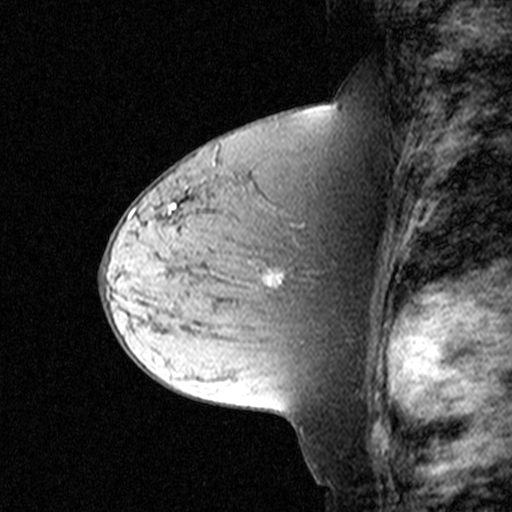
Breast MRI (dynamic contrast-enhanced), one sagittal slice. Position 21 of 44 along the scan axis. Dynamic contrast-enhanced study with each time point stored as its own series, time point 2 of 3 at this slice position (early post-contrast, ordered by acquisition time). 1.5 T. TE 4.5 ms, TR 11 ms. 3 mm slice thickness. 512 × 512 image matrix, field of view 200 × 200 mm. Patient: female, 44 years. Case-level facts recorded for this patient, not image findings: setting: breast cancer imaged before/during neoadjuvant chemotherapy; receptor status: triple-negative.
Structures marked on this image (semi-automatic segmentation, software-assisted and operator-edited):
- analysis volume of interest (the breast-tissue region the enhancement analysis was run in; not a lesion): box from (x=174, y=204) to (x=303, y=305) px
- tumour enhancement mask (voxels above the 90 % enhancement threshold inside the analysis volume of interest): (x=174, y=205)–(x=280, y=288)